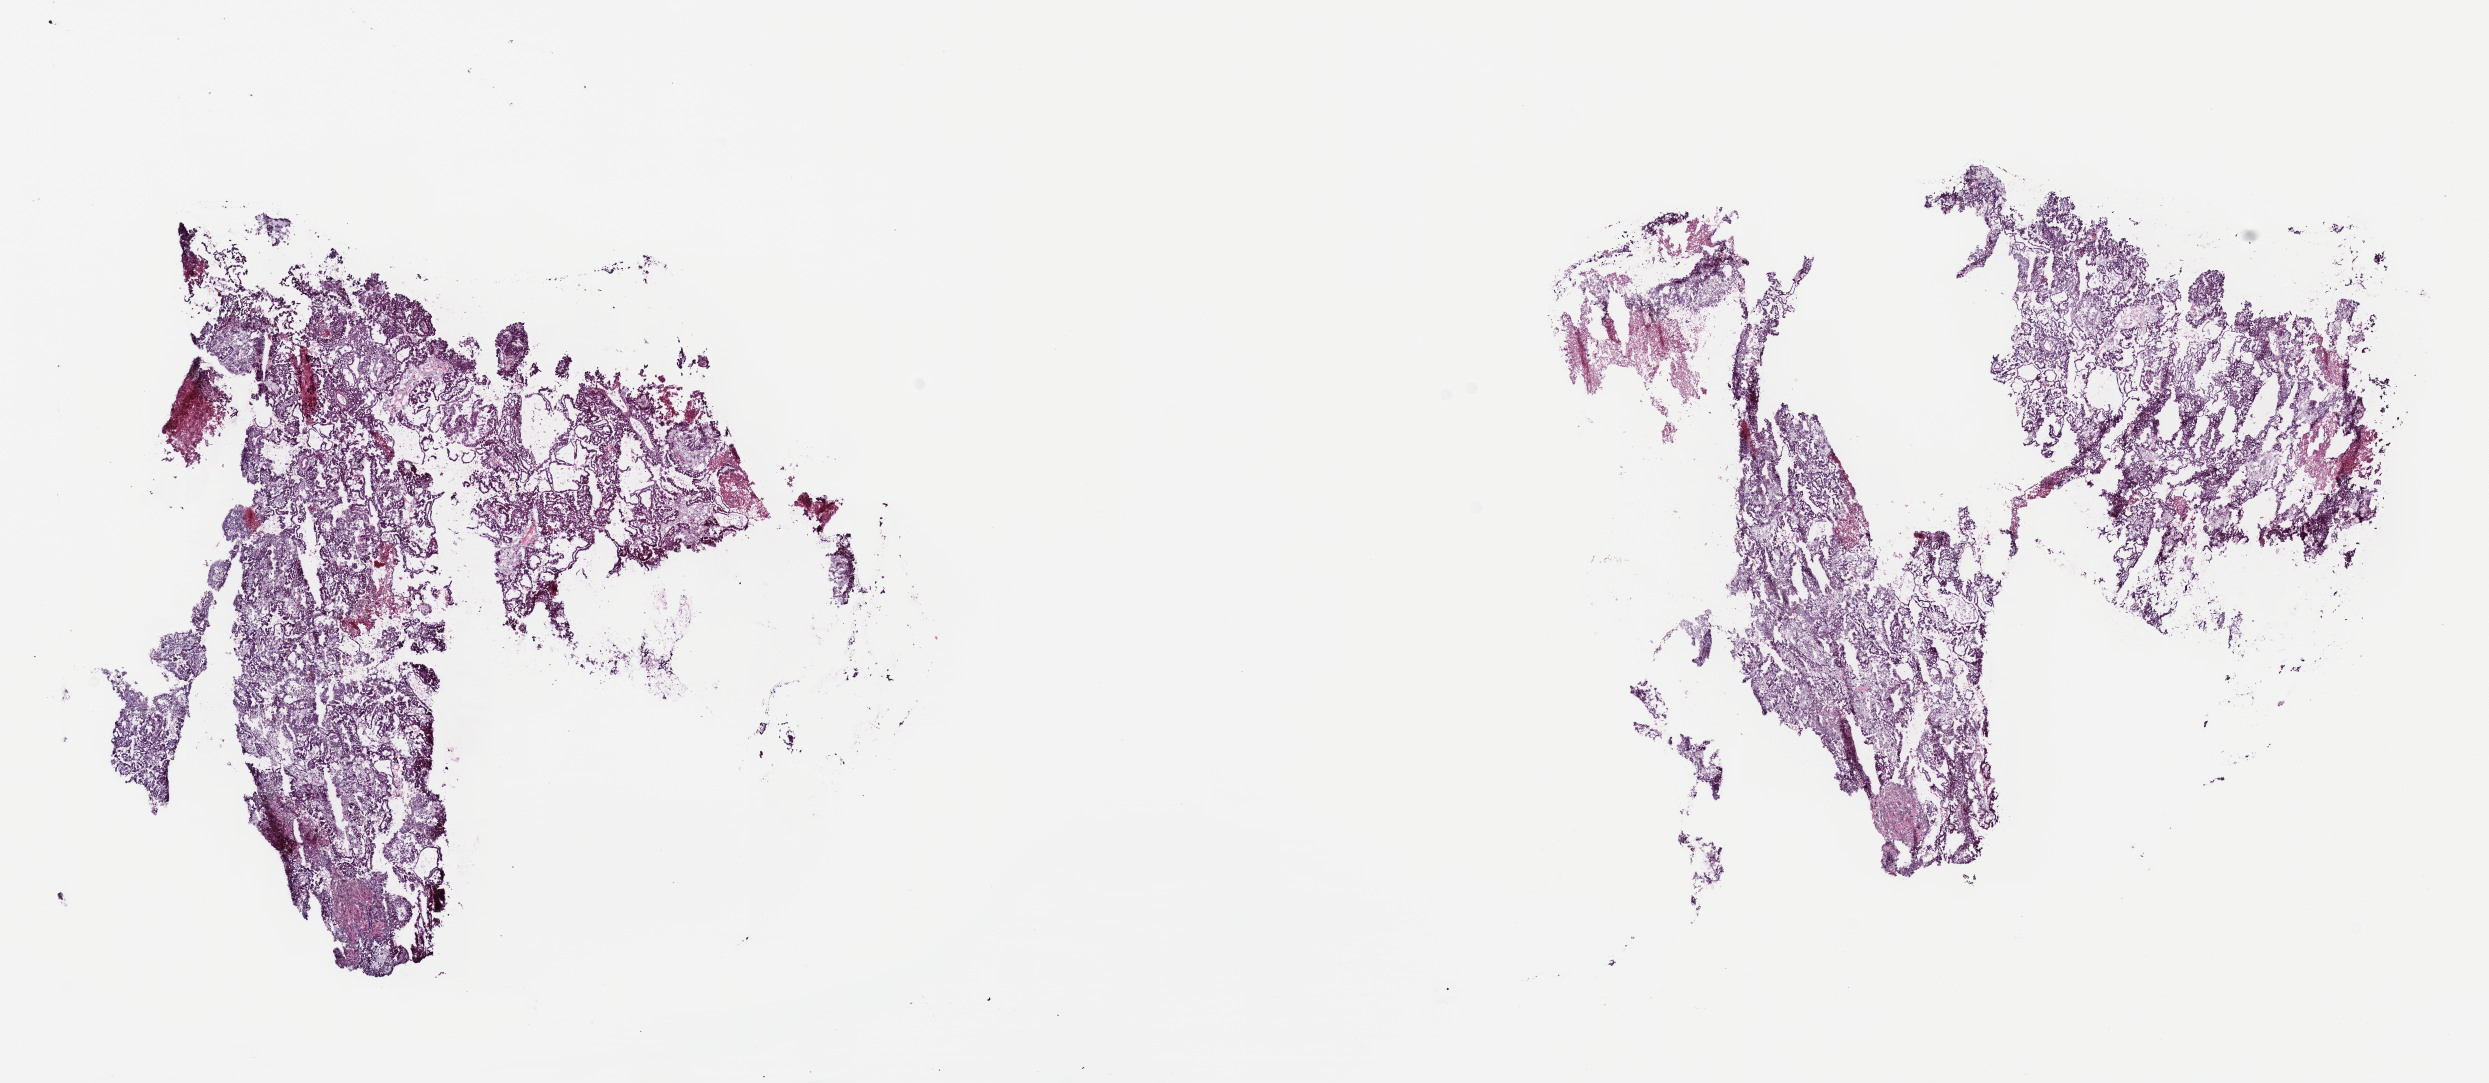
Digitized H&E tissue section (whole slide) — low-resolution overview of the scanned area, about 20.1 x 8.8 mm; frozen section from the top of the tissue portion; kidney, primary tumour sample. Patient: male, age at initial diagnosis 80 years. Composition of this section per pathologist review: tumour cells 95%, tumour nuclei 70%.
Pathologic diagnosis: Papillary adenocarcinoma, NOS.